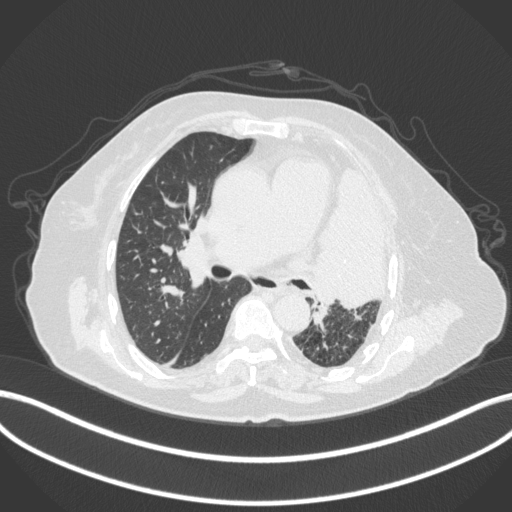
Chest CT, one axial slice. Slice 221 of 399 in the series (ordered by position). 120 kVp. Lung window (W 1500 / L -600 HU). 1 mm slice thickness. 512 × 512 image matrix, field of view 400 × 400 mm. Female patient, age 75 years. Case-level facts recorded for this patient, not image findings: clinical TNM (as recorded): T3 N3 M1.
Outlined on this slice (bounding box drawn by a radiologist):
- lung tumour (recorded histology: adenocarcinoma): bounding box (x1, y1, x2, y2) in pixels: (309, 160, 388, 307)